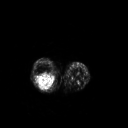
FDG PET of an extremity soft-tissue mass (from a PET/CT study), one axial slice; position 174 of 267 along the scan axis; 3.27 mm slice thickness; 128 × 128 image matrix. Patient: female, 62 years. Case-level facts recorded for this patient, not image findings: histological type: liposarcoma; site of the primary tumour: right thigh.
Outlined on this slice (expert contour drawn on MRI and transferred to this co-registered scan by the dataset authors):
- gross tumour volume (mass): bounding box <35,72,56,90> (left, top, right, bottom; pixels)